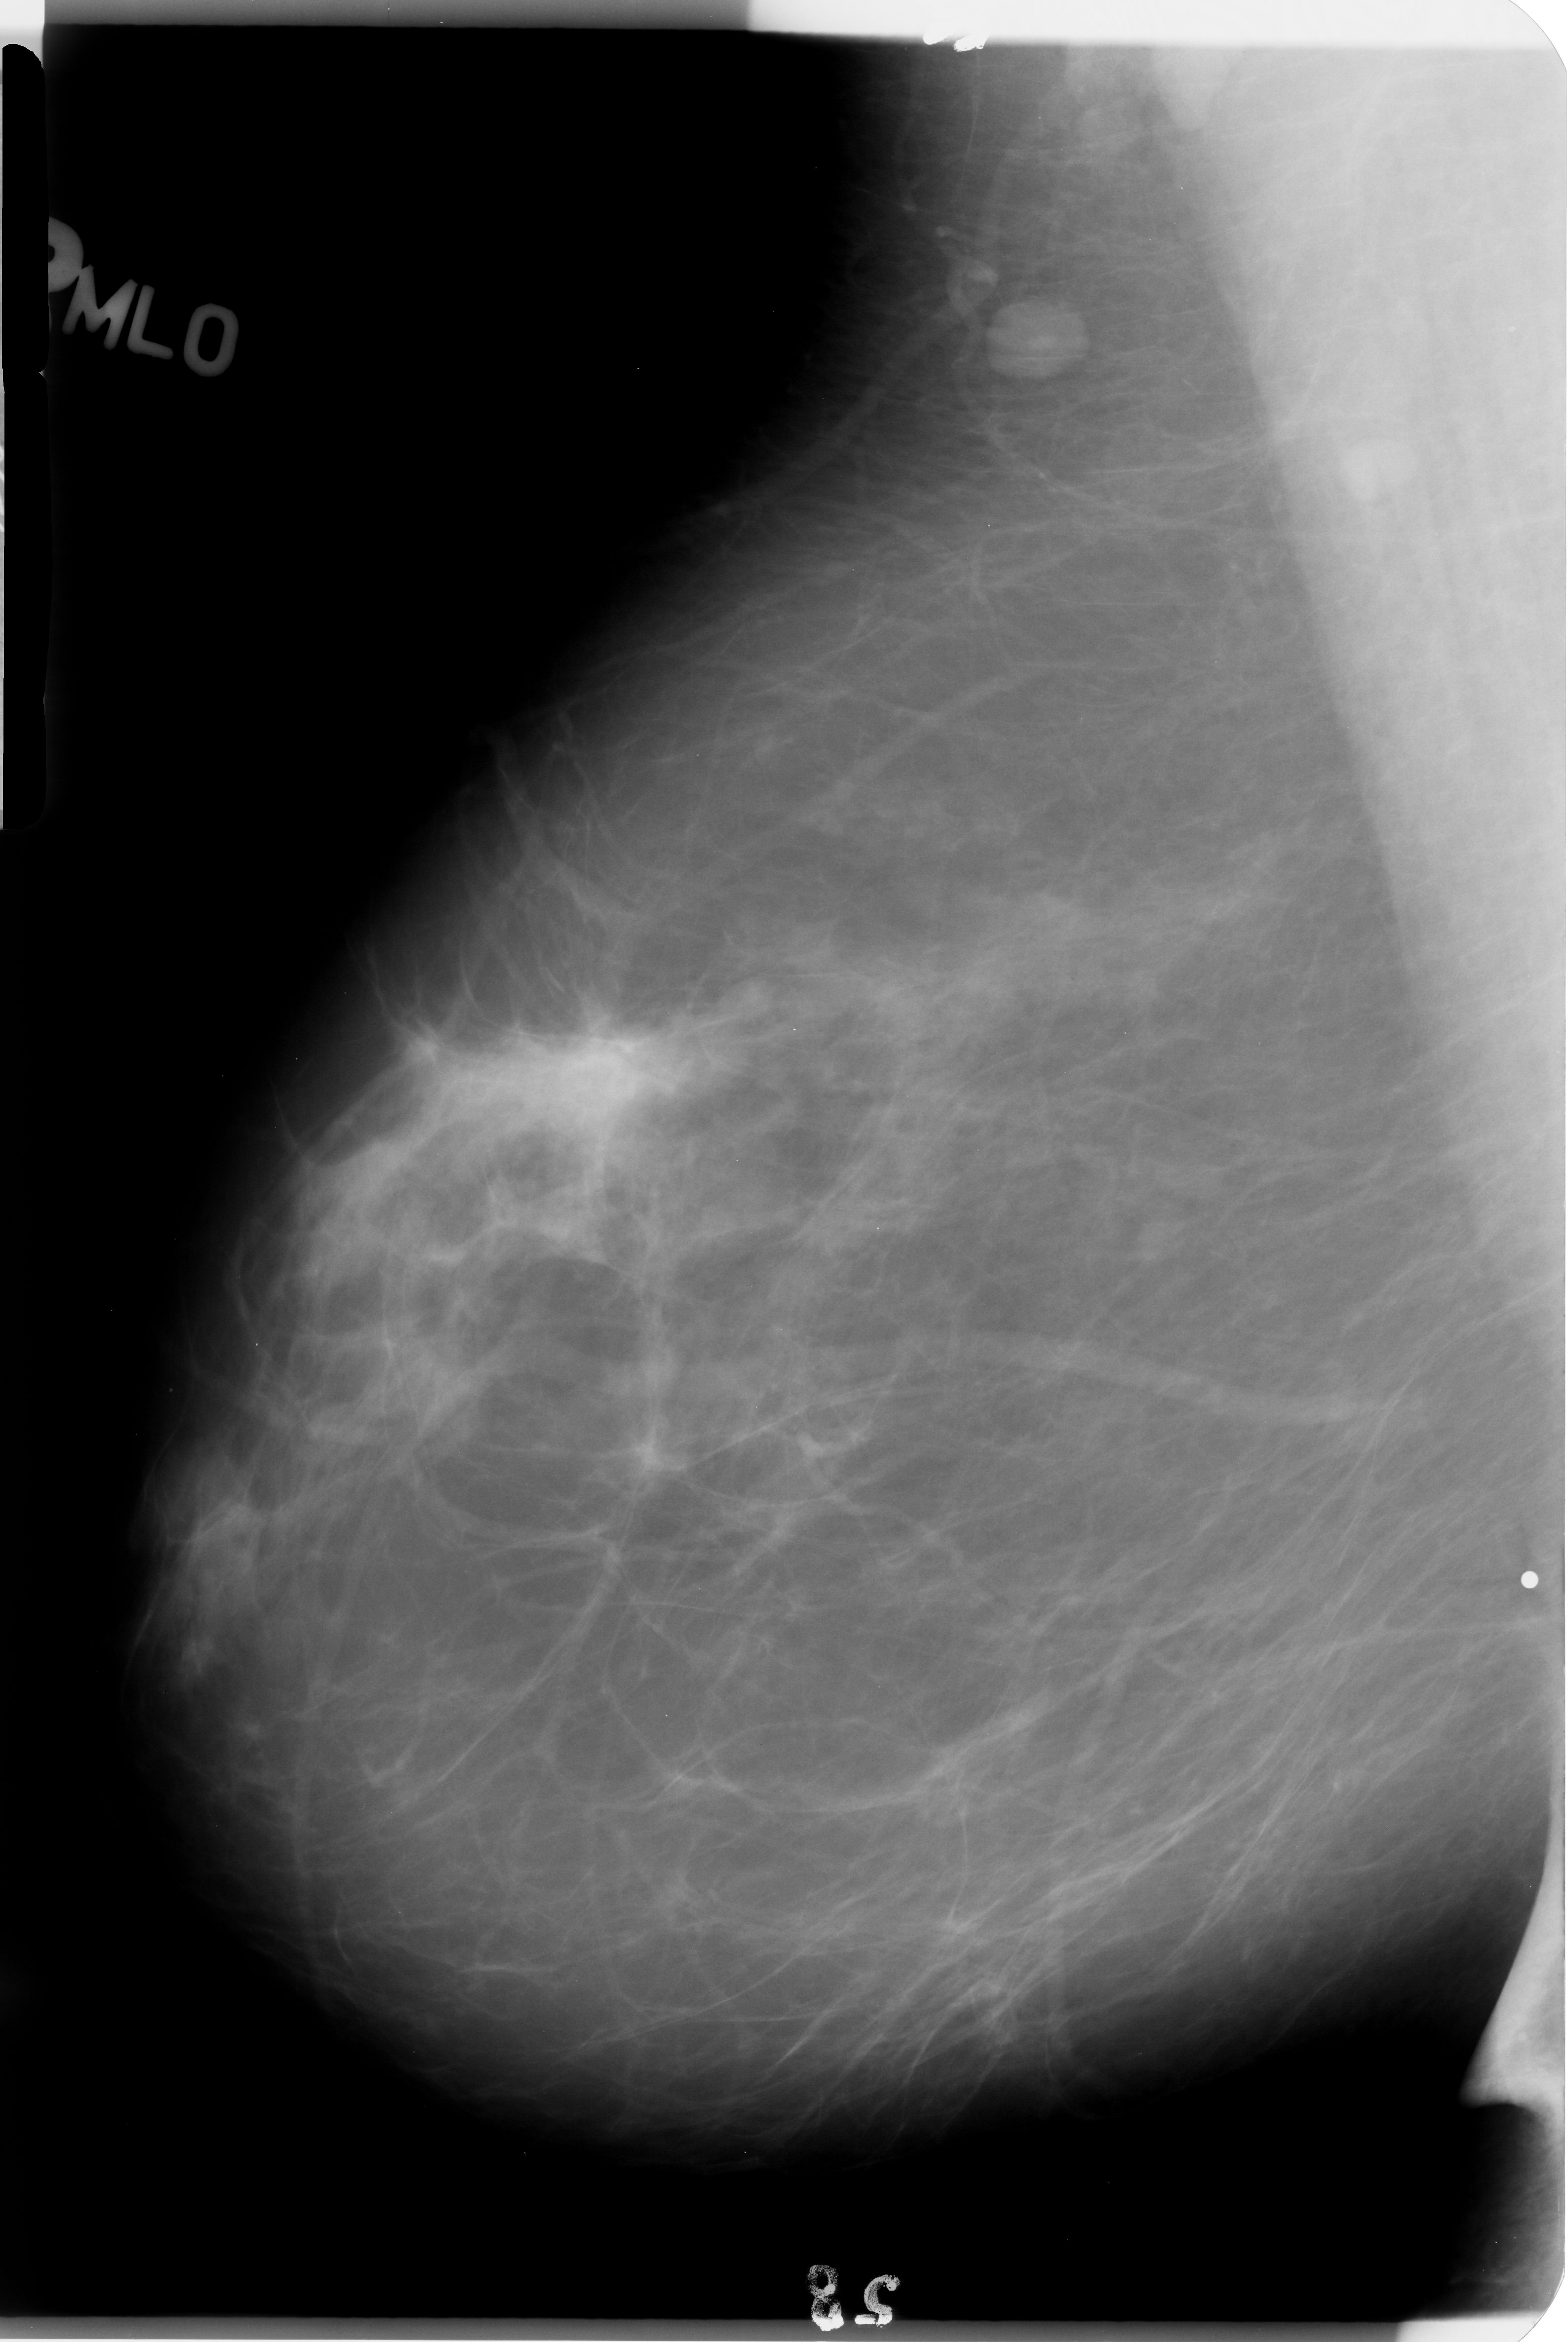
Digitized screen-film mammogram; right breast; mediolateral oblique (MLO) view; BI-RADS breast density category 2 (scale 1–4); 1568 × 2342 image matrix.
Expert-marked regions of interest on this image (one box per marked abnormality):
- mass, shape irregular, margins ill defined; BI-RADS assessment category 4; pathology (as recorded): benign: bounding box (x1, y1, x2, y2) in pixels: (149, 1478, 275, 1624)